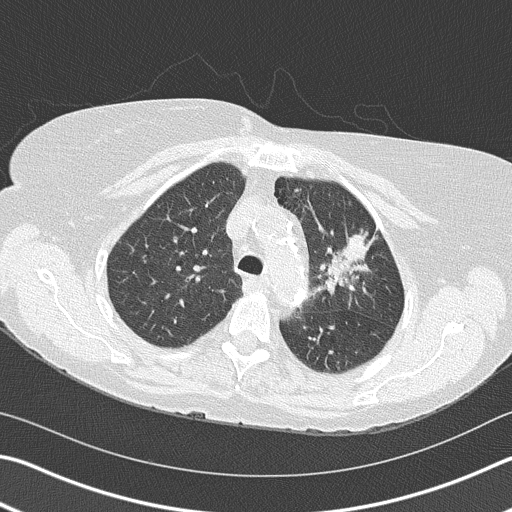
Chest CT (low-dose screening protocol), one axial image. Second annual screen. Lung window (W 1500 / L -600 HU). 2 mm slice thickness. Lung (sharp) reconstruction kernel (B50f). 512 × 512 image matrix. Female participant, aged 68 years at enrolment. Former smoker at enrolment.
Lesion marked by an expert reader, bounding box (x1, y1, x2, y2) in pixels: (293, 209, 387, 315). The exam's reader record, not a measurement of the box and not confirmed to be the same lesion: non-calcified nodule or mass ≥4 mm, left upper lobe, 4 × 2 mm, spiculated (stellate) margins, soft tissue attenuation, pre-existing on the prior screen: yes; interval growth: yes. Lung cancer was diagnosed 392 days after this screen (after the third annual screen): adenocarcinoma, NOS, left upper lobe, poorly differentiated (G3), stage IB (AJCC 6th edition), 50 mm at pathology.